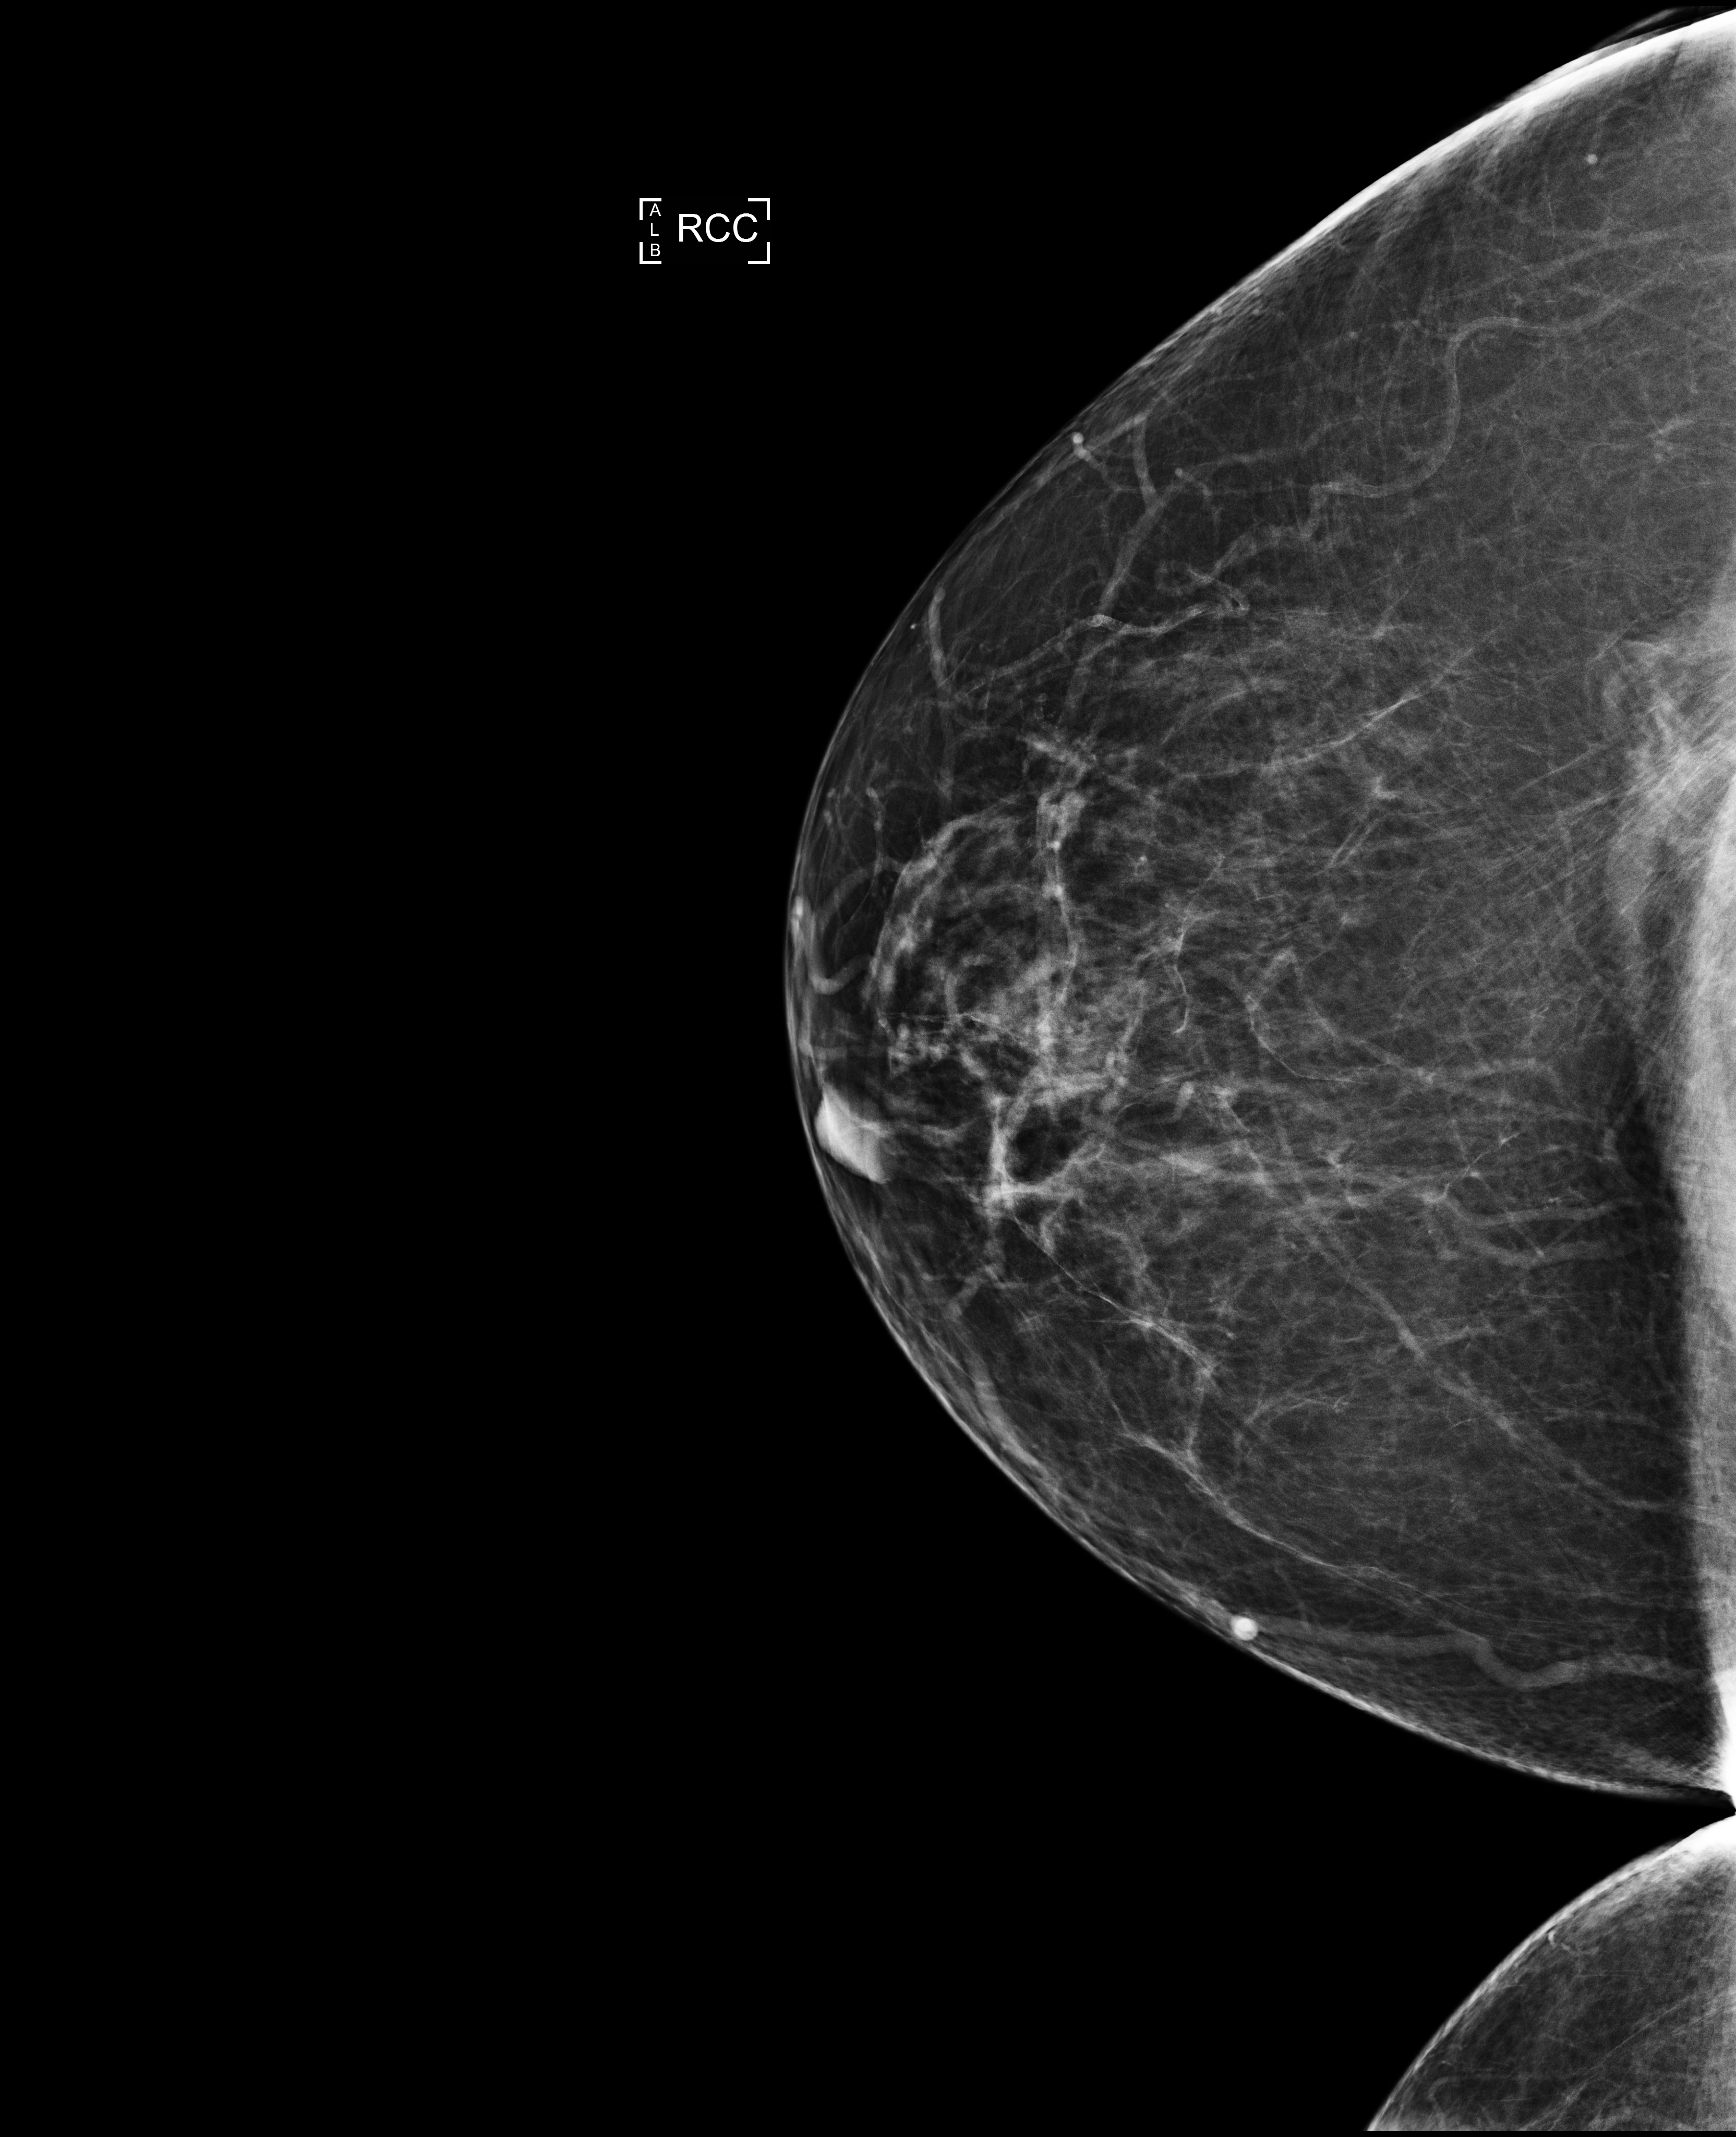
Annual screening mammography examination, compressed breast thickness 78 mm. Patient: female, 62 years.
Image type: full-field digital mammogram. Breast: right. Projection: CC view.